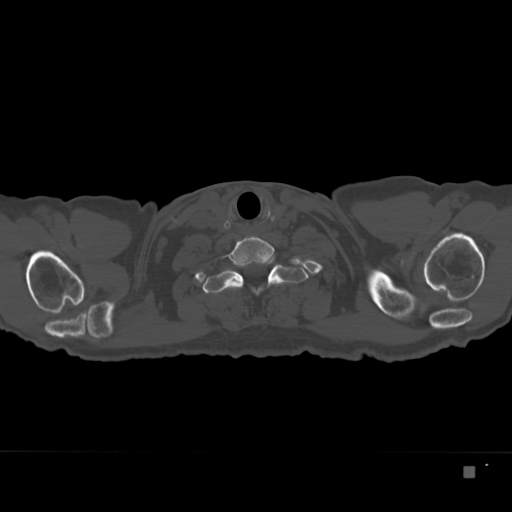
CT including the spine, one axial slice. Position 321 of 332 along the scan axis. Reconstruction kernel Br40s. Bone window (W 1800 / L 400 HU). 1.5 mm slice thickness. 512 × 512 image matrix. Patient: male, 72 years. From the clinical record (not read from this slice): primary cancer: skeletal.
Outlined on this slice (semi-automatically segmented with operator editing):
- T1 vertebra: bounding box (x1, y1, x2, y2) in pixels: (202, 255, 309, 296)